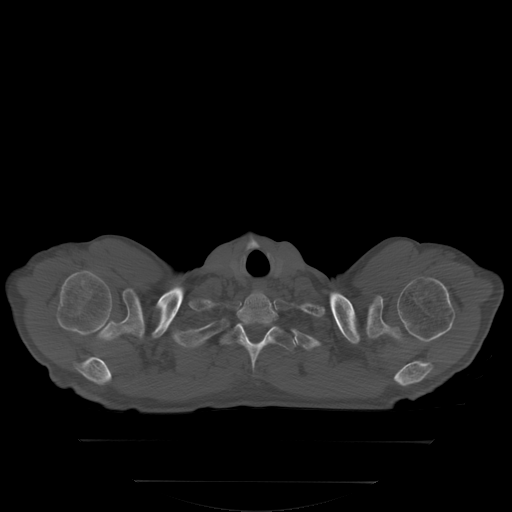
CT including the spine, one axial slice. Position 291 of 350 along the scan axis. Bone window (W 1800 / L 400 HU). 2.5 mm slice thickness. 512 × 512 image matrix, field of view 500 × 500 mm. Patient: male, 58 years. From the clinical record (not read from this slice): primary cancer: prostate; vertebrae with lytic lesions (as recorded): L1.
Outlined on this slice (semi-automatically segmented with operator editing):
- T1 vertebra: bounding box <225,321,298,370> (left, top, right, bottom; pixels)